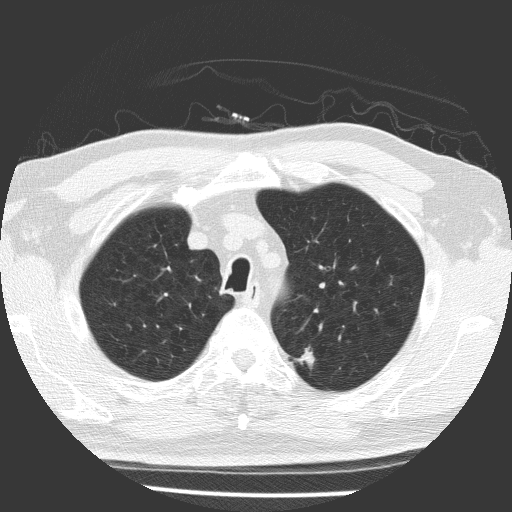
Axial slice from a low-dose chest CT screening exam; baseline annual screen; lung window (W 1500 / L -600 HU); 2 mm slice thickness; lung (sharp) reconstruction kernel (FC51); 512 × 512 image matrix, field of view 323 × 323 mm. Male, age 64 years at enrolment. Former smoker at enrolment.
Expert reader's lesion annotation, bounding box [x1, y1, x2, y2] px = [285, 340, 326, 378]. Screening reader's record for this exam (one nodule recorded; not confirmed to be the boxed lesion): non-calcified nodule or mass ≥4 mm, left upper lobe, 9 × 7 mm, spiculated (stellate) margins, soft tissue attenuation. Official screen result: positive, change unspecified: nodule(s) >= 4 mm or enlarging nodule(s), mass(es), or other non-specific abnormalities suspicious for lung cancer.